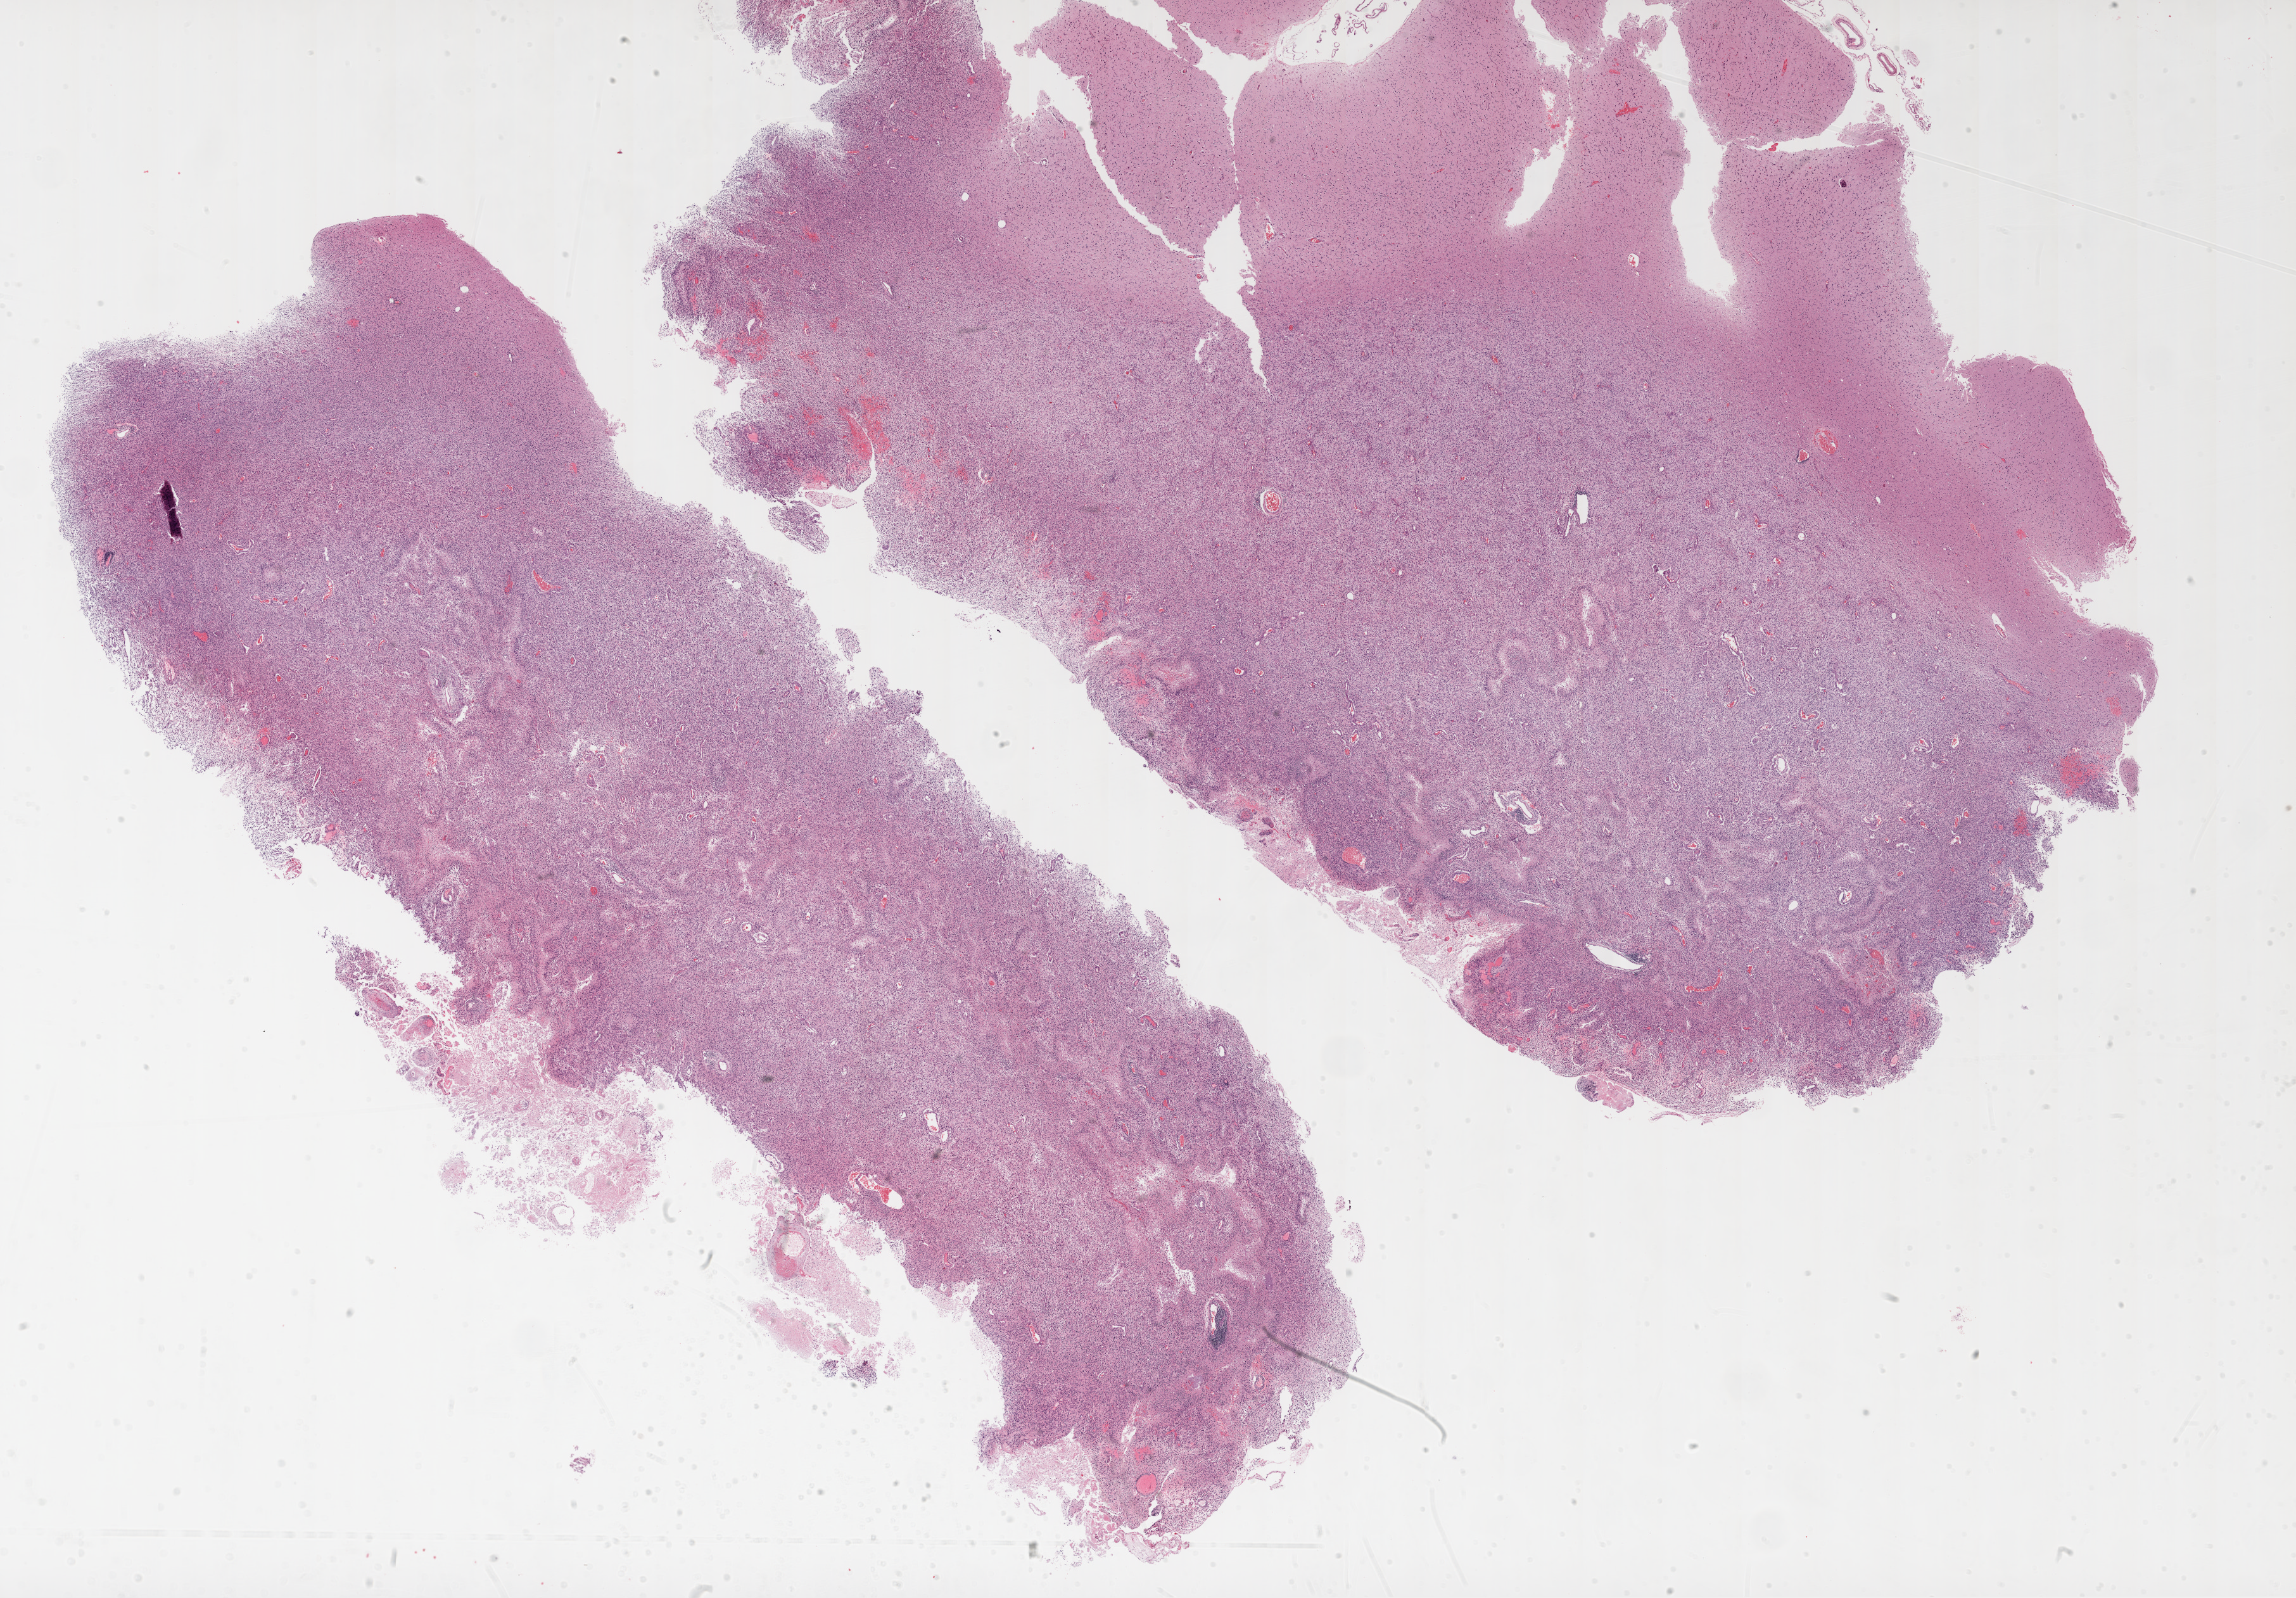
Digitized H&E-stained tissue section (whole slide), shown as a low-resolution overview of the whole scanned area (about 29.1 x 20.2 mm, acquisition: 20x scan); formalin-fixed paraffin-embedded (FFPE) diagnostic section; brain, primary tumour sample. Patient: male, age at initial diagnosis 60 years.
Diagnosis: Glioblastoma.